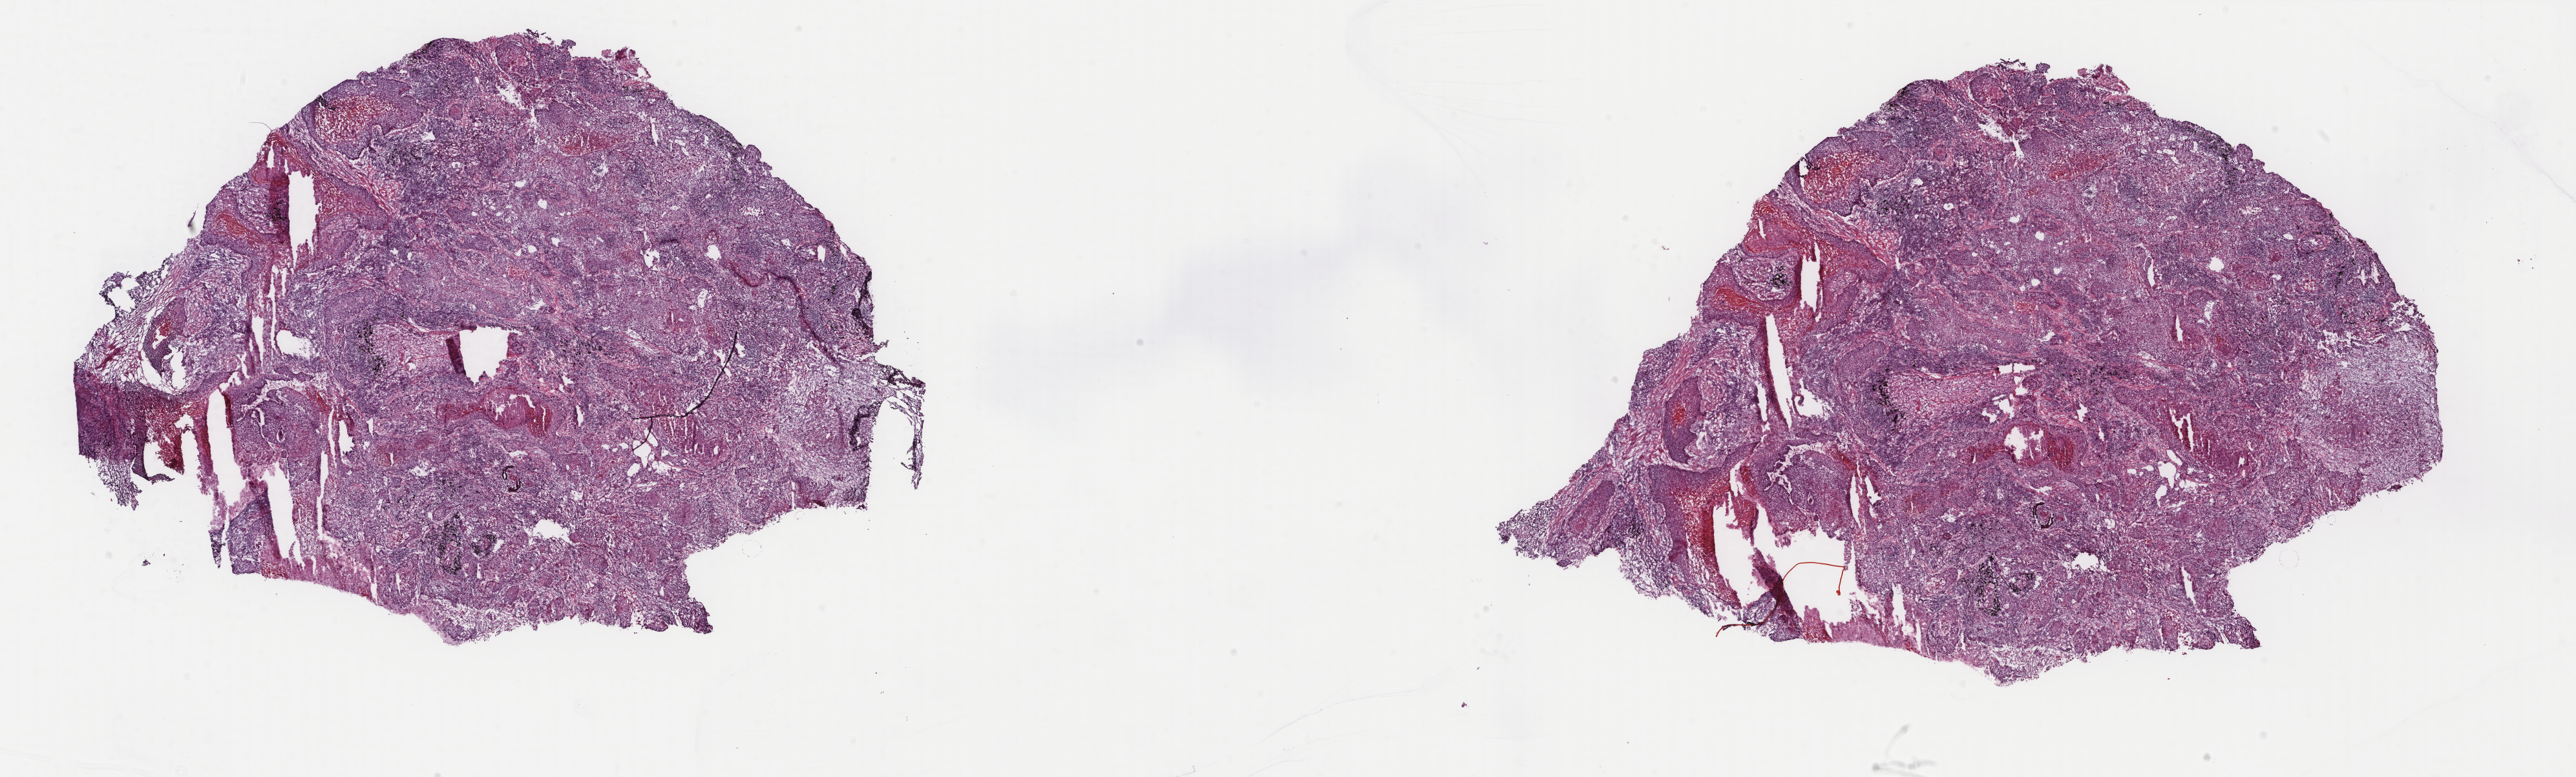
H&E whole-slide image, a low-resolution overview of the entire scanned area, about 31.6 x 9.5 mm (acquisition: 40x scan). Frozen section from the top of the tissue portion. Sample: primary tumour, lung. Male patient; age at initial diagnosis 68 years. Slide review estimates, as recorded: tumour cells 60%, tumour nuclei 70%, normal cells 0%, stromal cells 30%, necrosis 10%. Inflammatory infiltration, as recorded: lymphocyte infiltration 0%, monocyte infiltration 0%, neutrophil infiltration 0%.
* laterality: left
* histologic diagnosis: Squamous cell carcinoma, NOS (lower lobe, lung)
* AJCC pathologic stage: IB